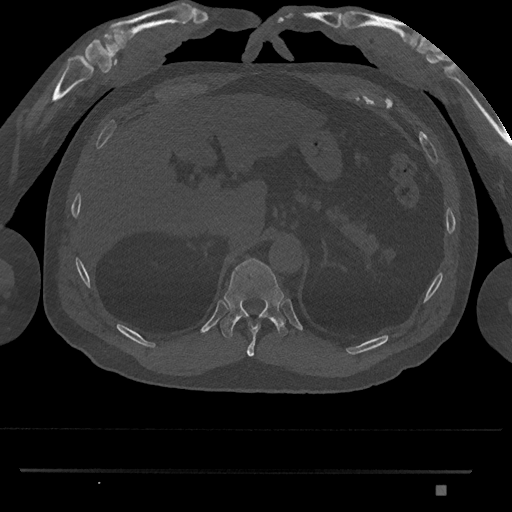
CT including the spine, one axial slice. Slice 964 of 1134 in the series (ordered by position). Reconstruction kernel Br40s/3. 120 kVp. Bone window (W 1800 / L 400 HU). 0.5 mm slice thickness. 512 × 512 image matrix, field of view 429 × 429 mm. Male patient, age 65 years. From the clinical record (not read from this slice): primary cancer: prostate.
Annotated regions visible in this slice (semi-automatically segmented with operator editing):
- T10 vertebra: bounding box <247,321,260,357> (left, top, right, bottom; pixels)
- T11 vertebra: <220,258,288,339>